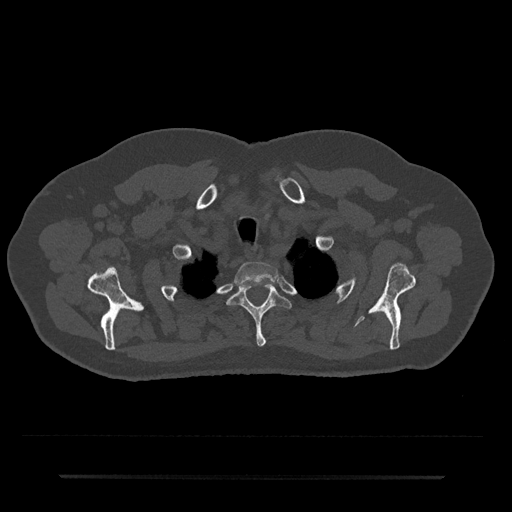
CT including the spine, one axial slice. 120 kVp. Bone window (W 1800 / L 400 HU). 0.5 mm slice thickness. 512 × 512 image matrix. Patient: male, 69 years. Case-level facts recorded for this patient, not image findings: primary cancer: prostate.
Annotated regions visible in this slice (semi-automatic segmentation, software-assisted and operator-edited):
- T1 vertebra: bounding box <234,262,279,286> (left, top, right, bottom; pixels)
- T2 vertebra: <227,282,292,347>